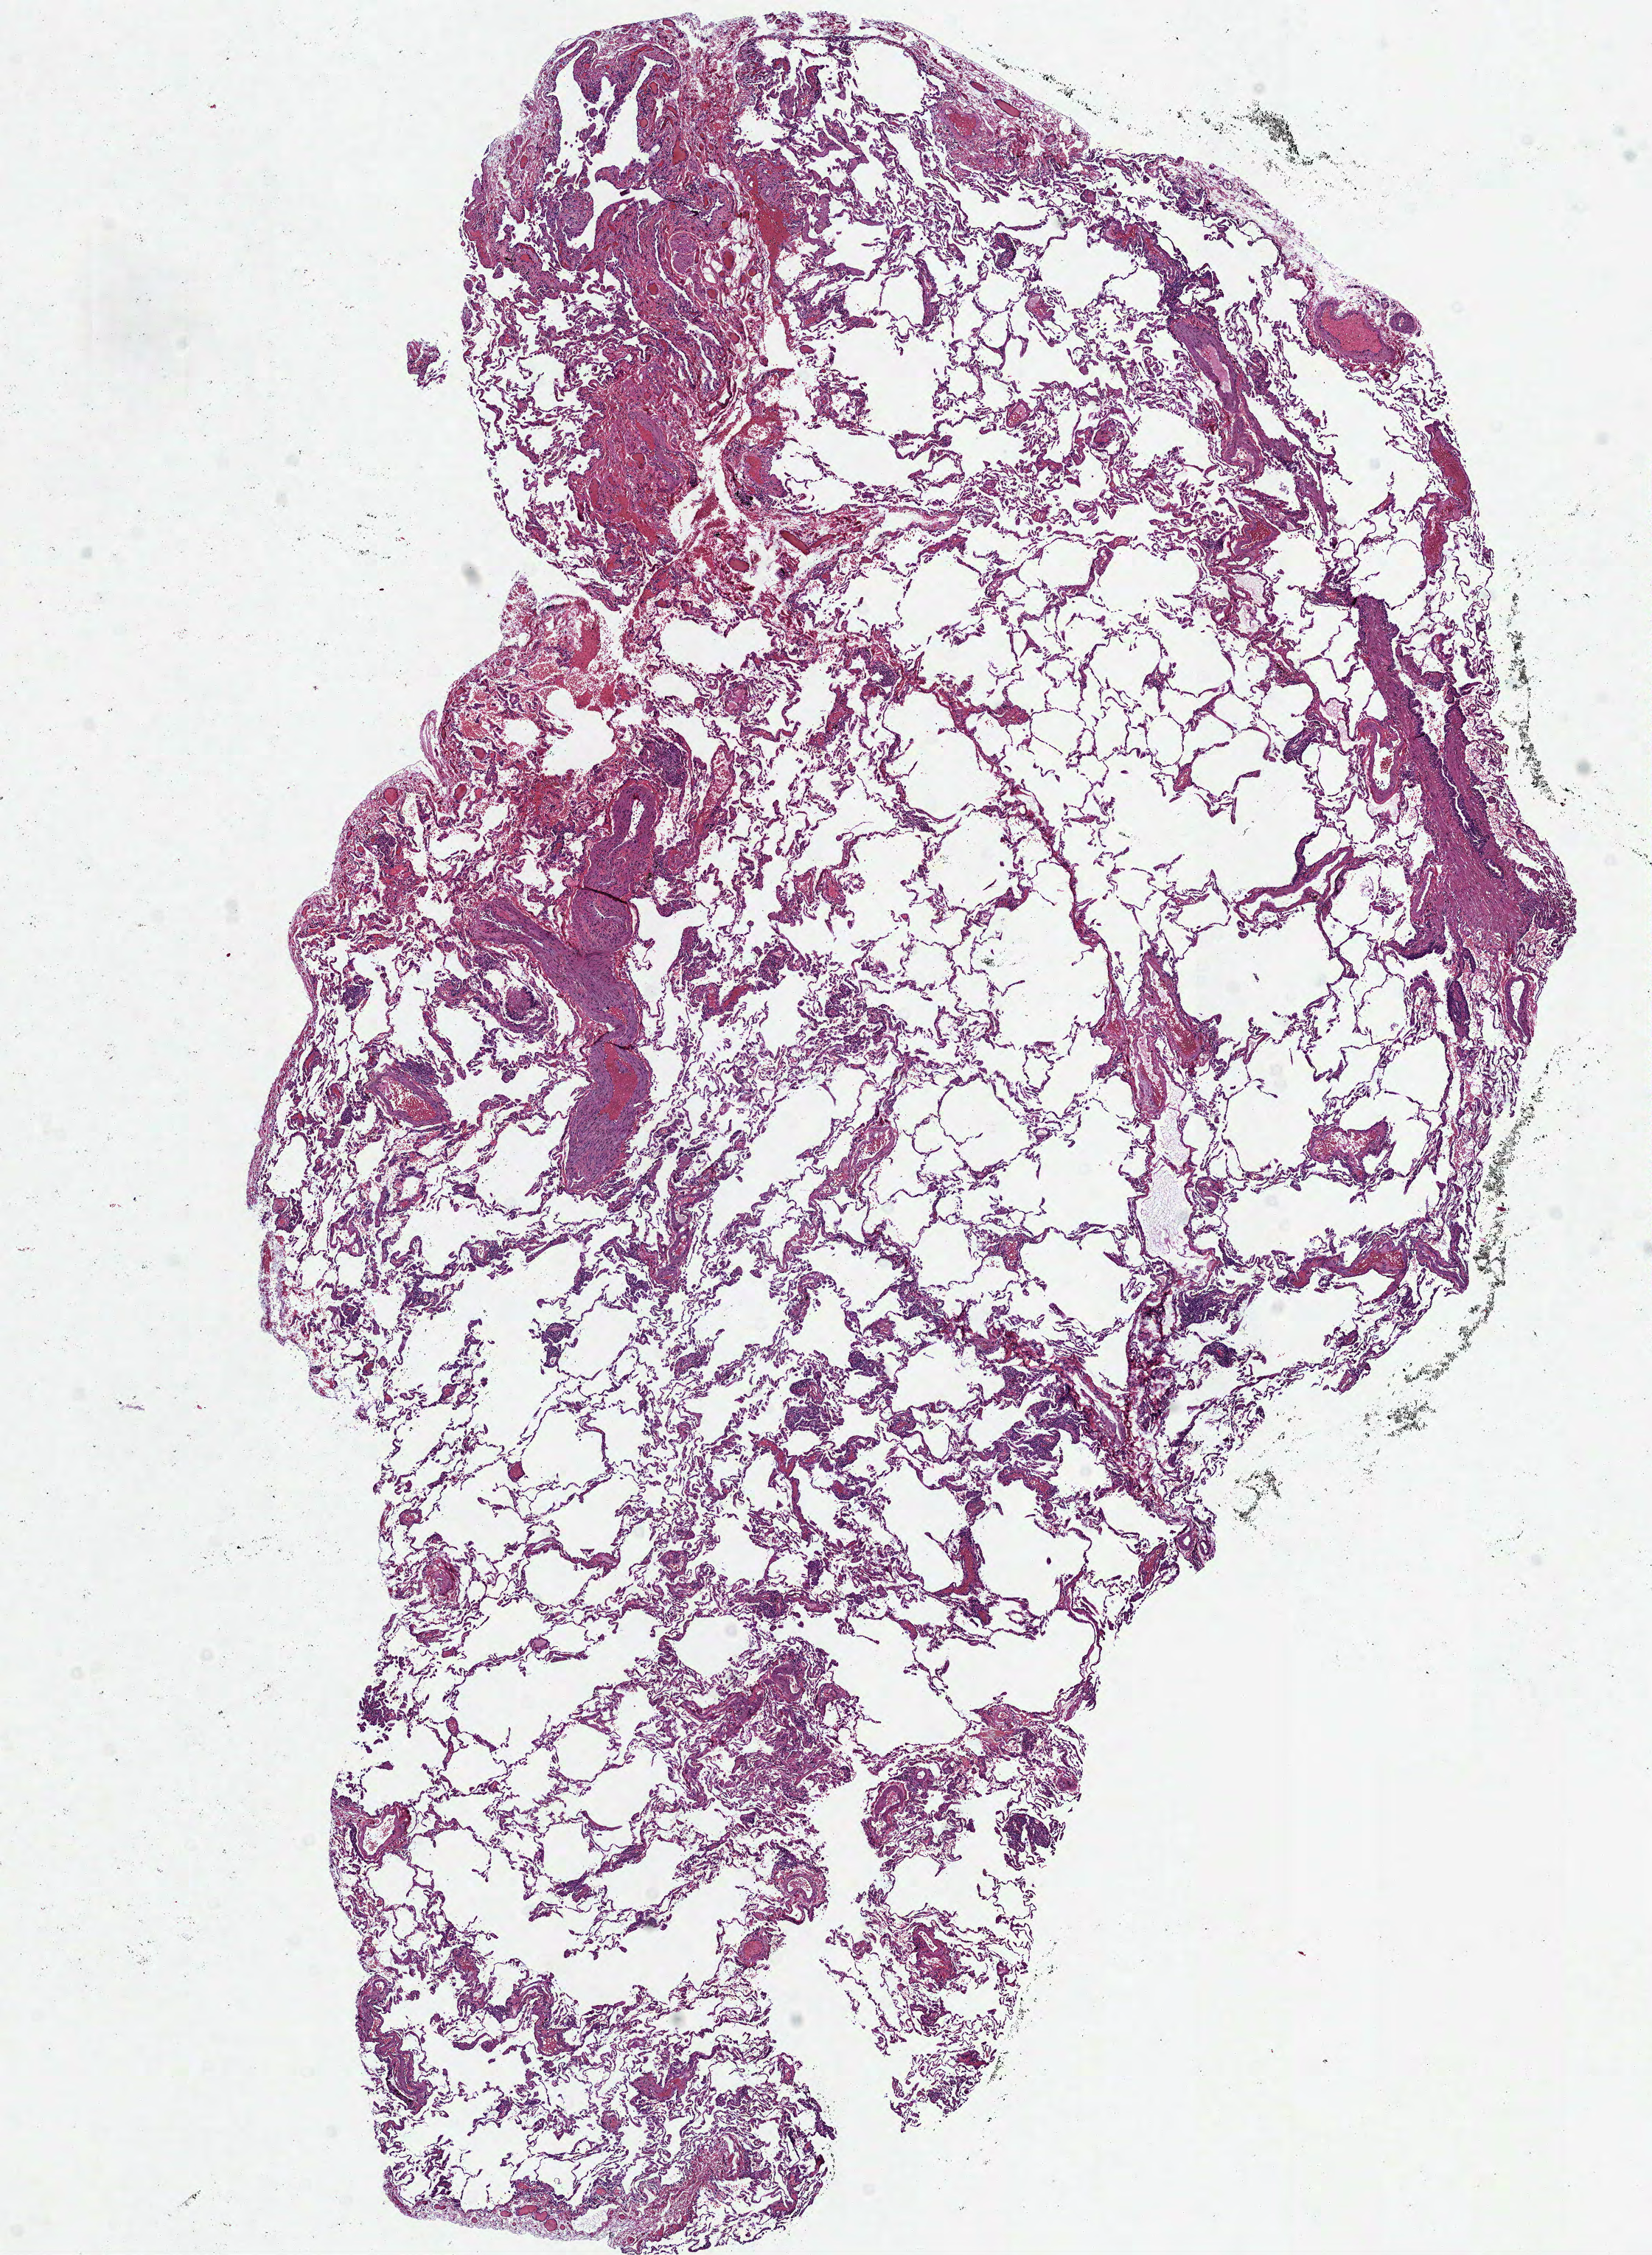
Digitized H&E-stained tissue section (whole slide) — low-resolution overview of the scanned area, about 9.0 x 12.3 mm; frozen section; solid tissue normal (non-tumour tissue) sample from the lung. Patient: male, age at initial diagnosis 64 years.
This section: solid tissue normal (non-tumour) sample from the same patient. Patient diagnosis: Mucinous adenocarcinoma (lower lobe, lung).